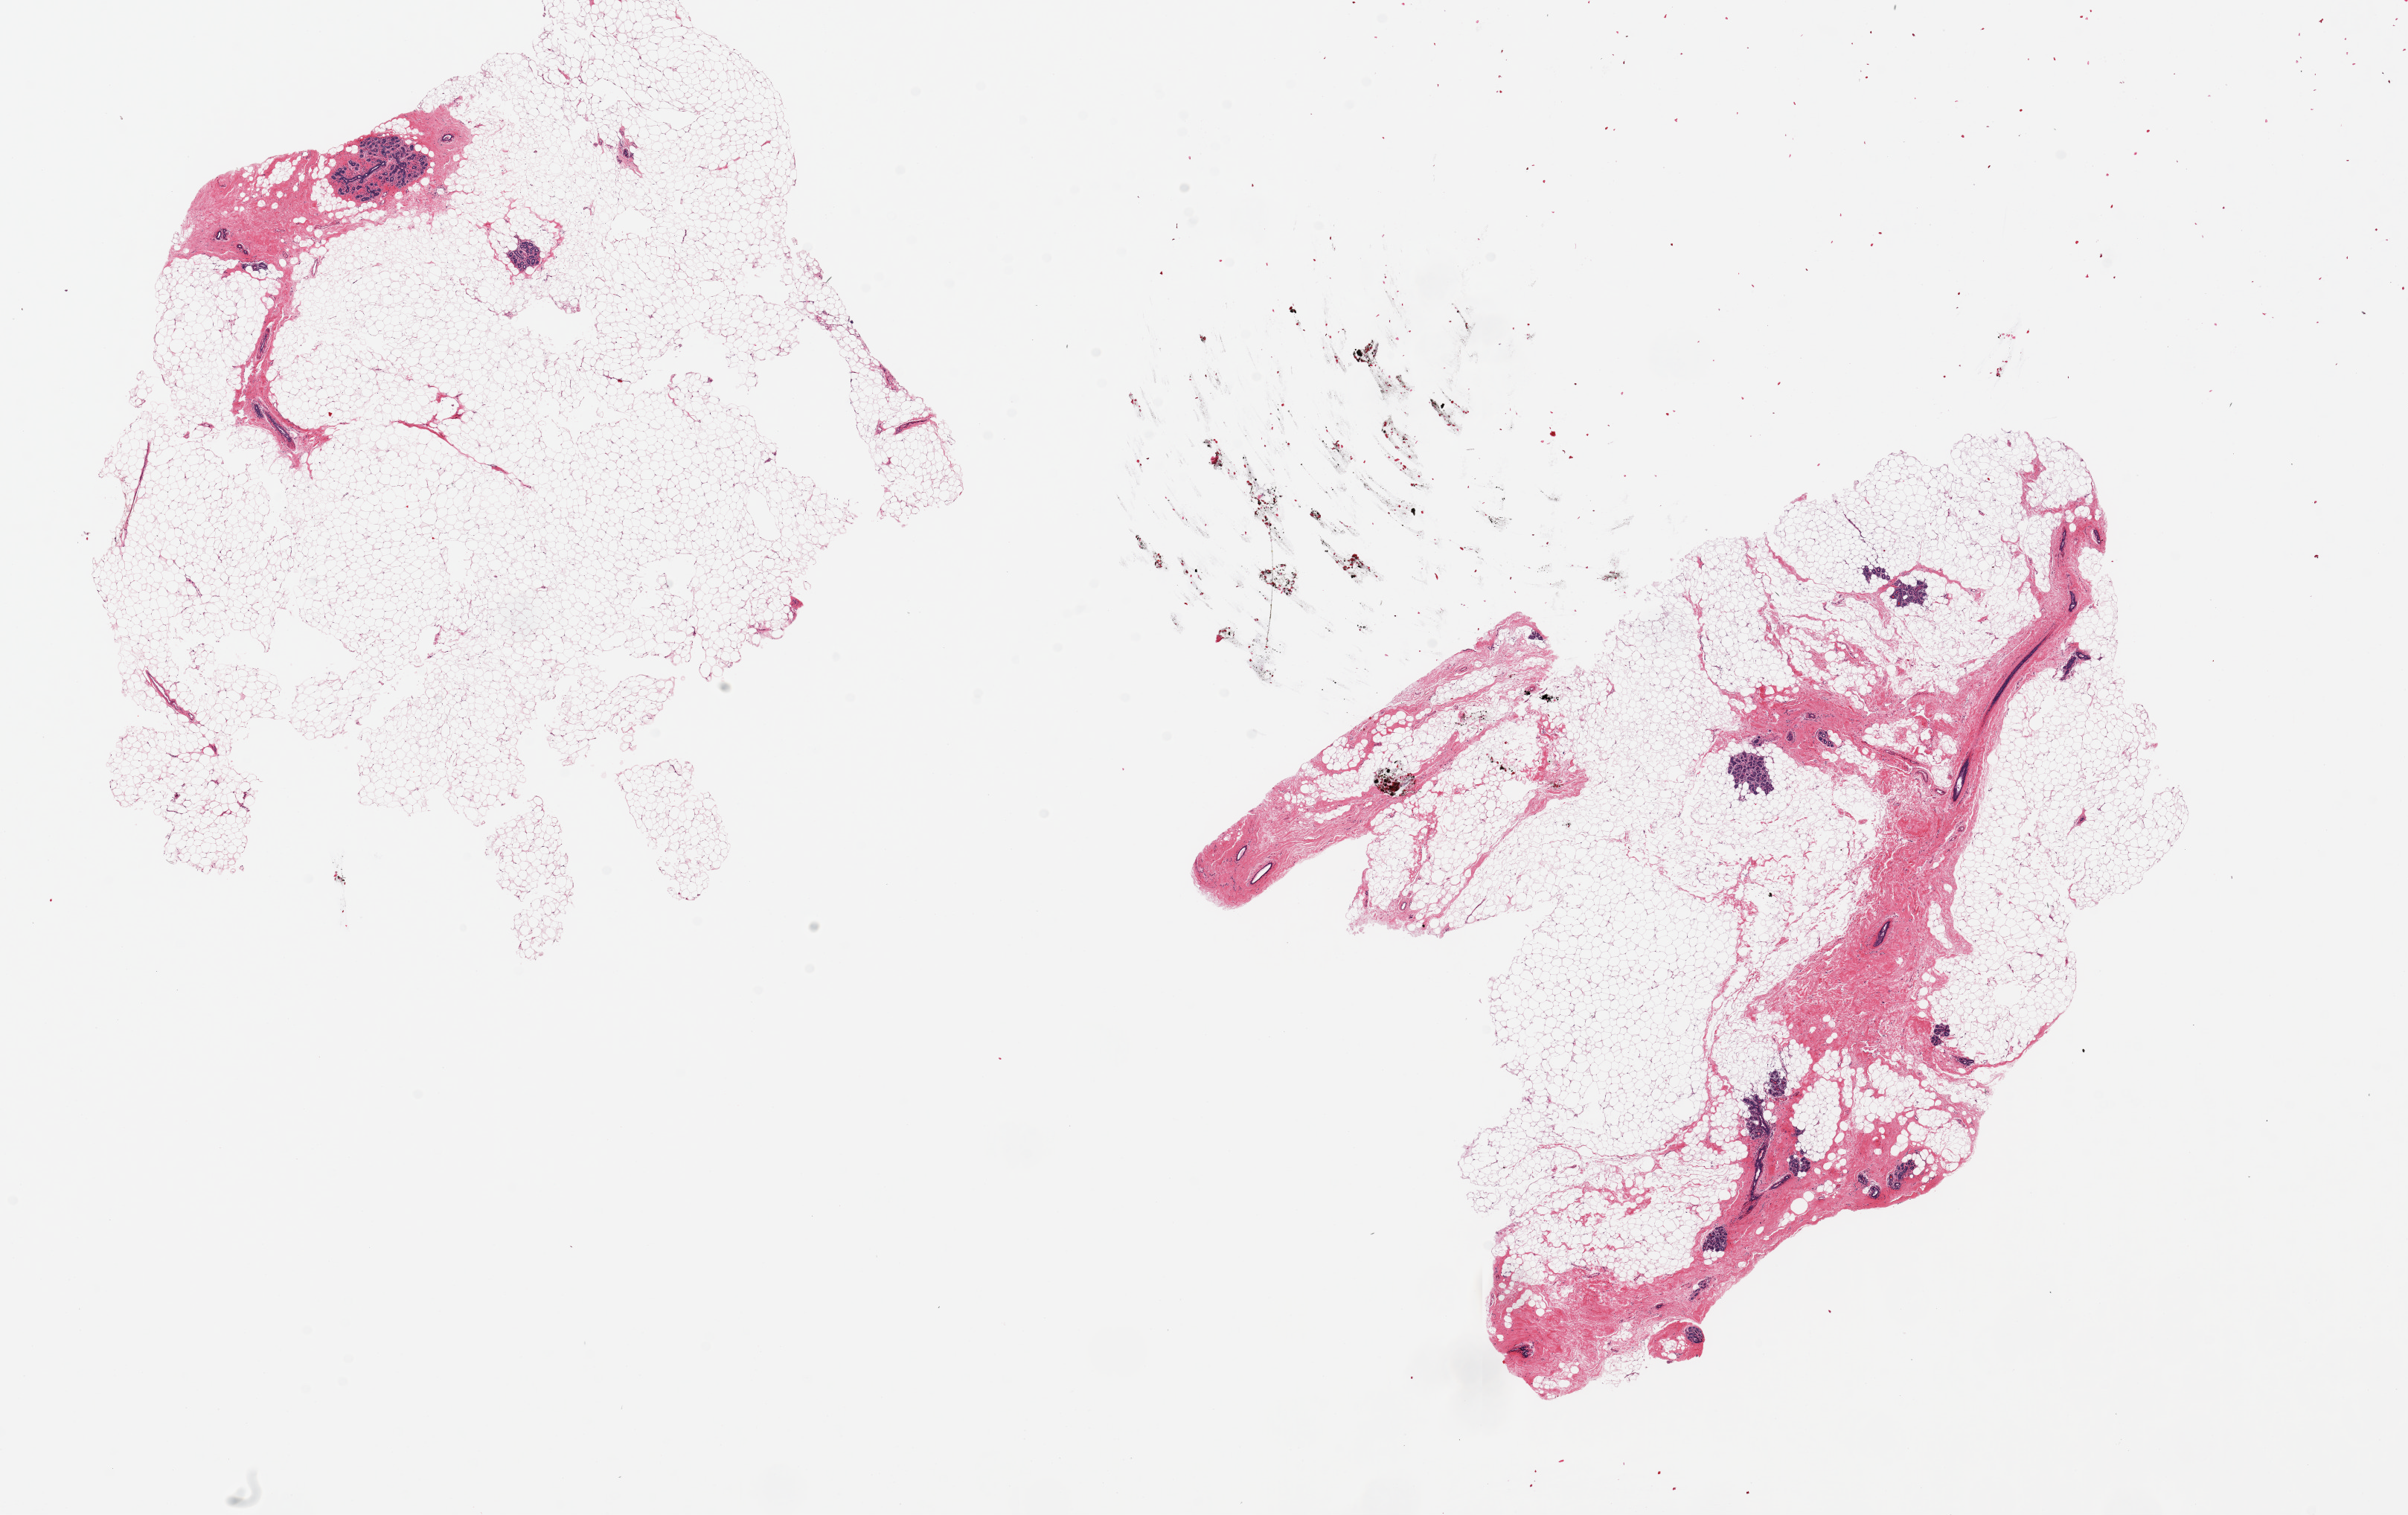
Whole-slide image, hematoxylin and eosin (H&E) stain — low-resolution overview of the scanned area, about 25.6 x 16.1 mm (slide scanned at 20x). PAXgene-fixed paraffin-embedded (PFPE) section. Section of breast (target tissue). Donor tissue sample. Female donor.
Review note (as recorded): 2 pieces ~10x6mm, rare atrophic TDLUs.